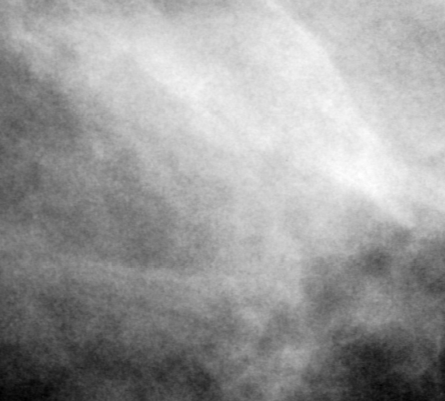
Region of interest cut from a scanned film mammogram (one marked finding); right breast; MLO view; BI-RADS breast density category 3 (scale 1–4).
Mass, shape round, margins obscured; BI-RADS assessment category 4; pathology result (as recorded, not read from the image): benign.